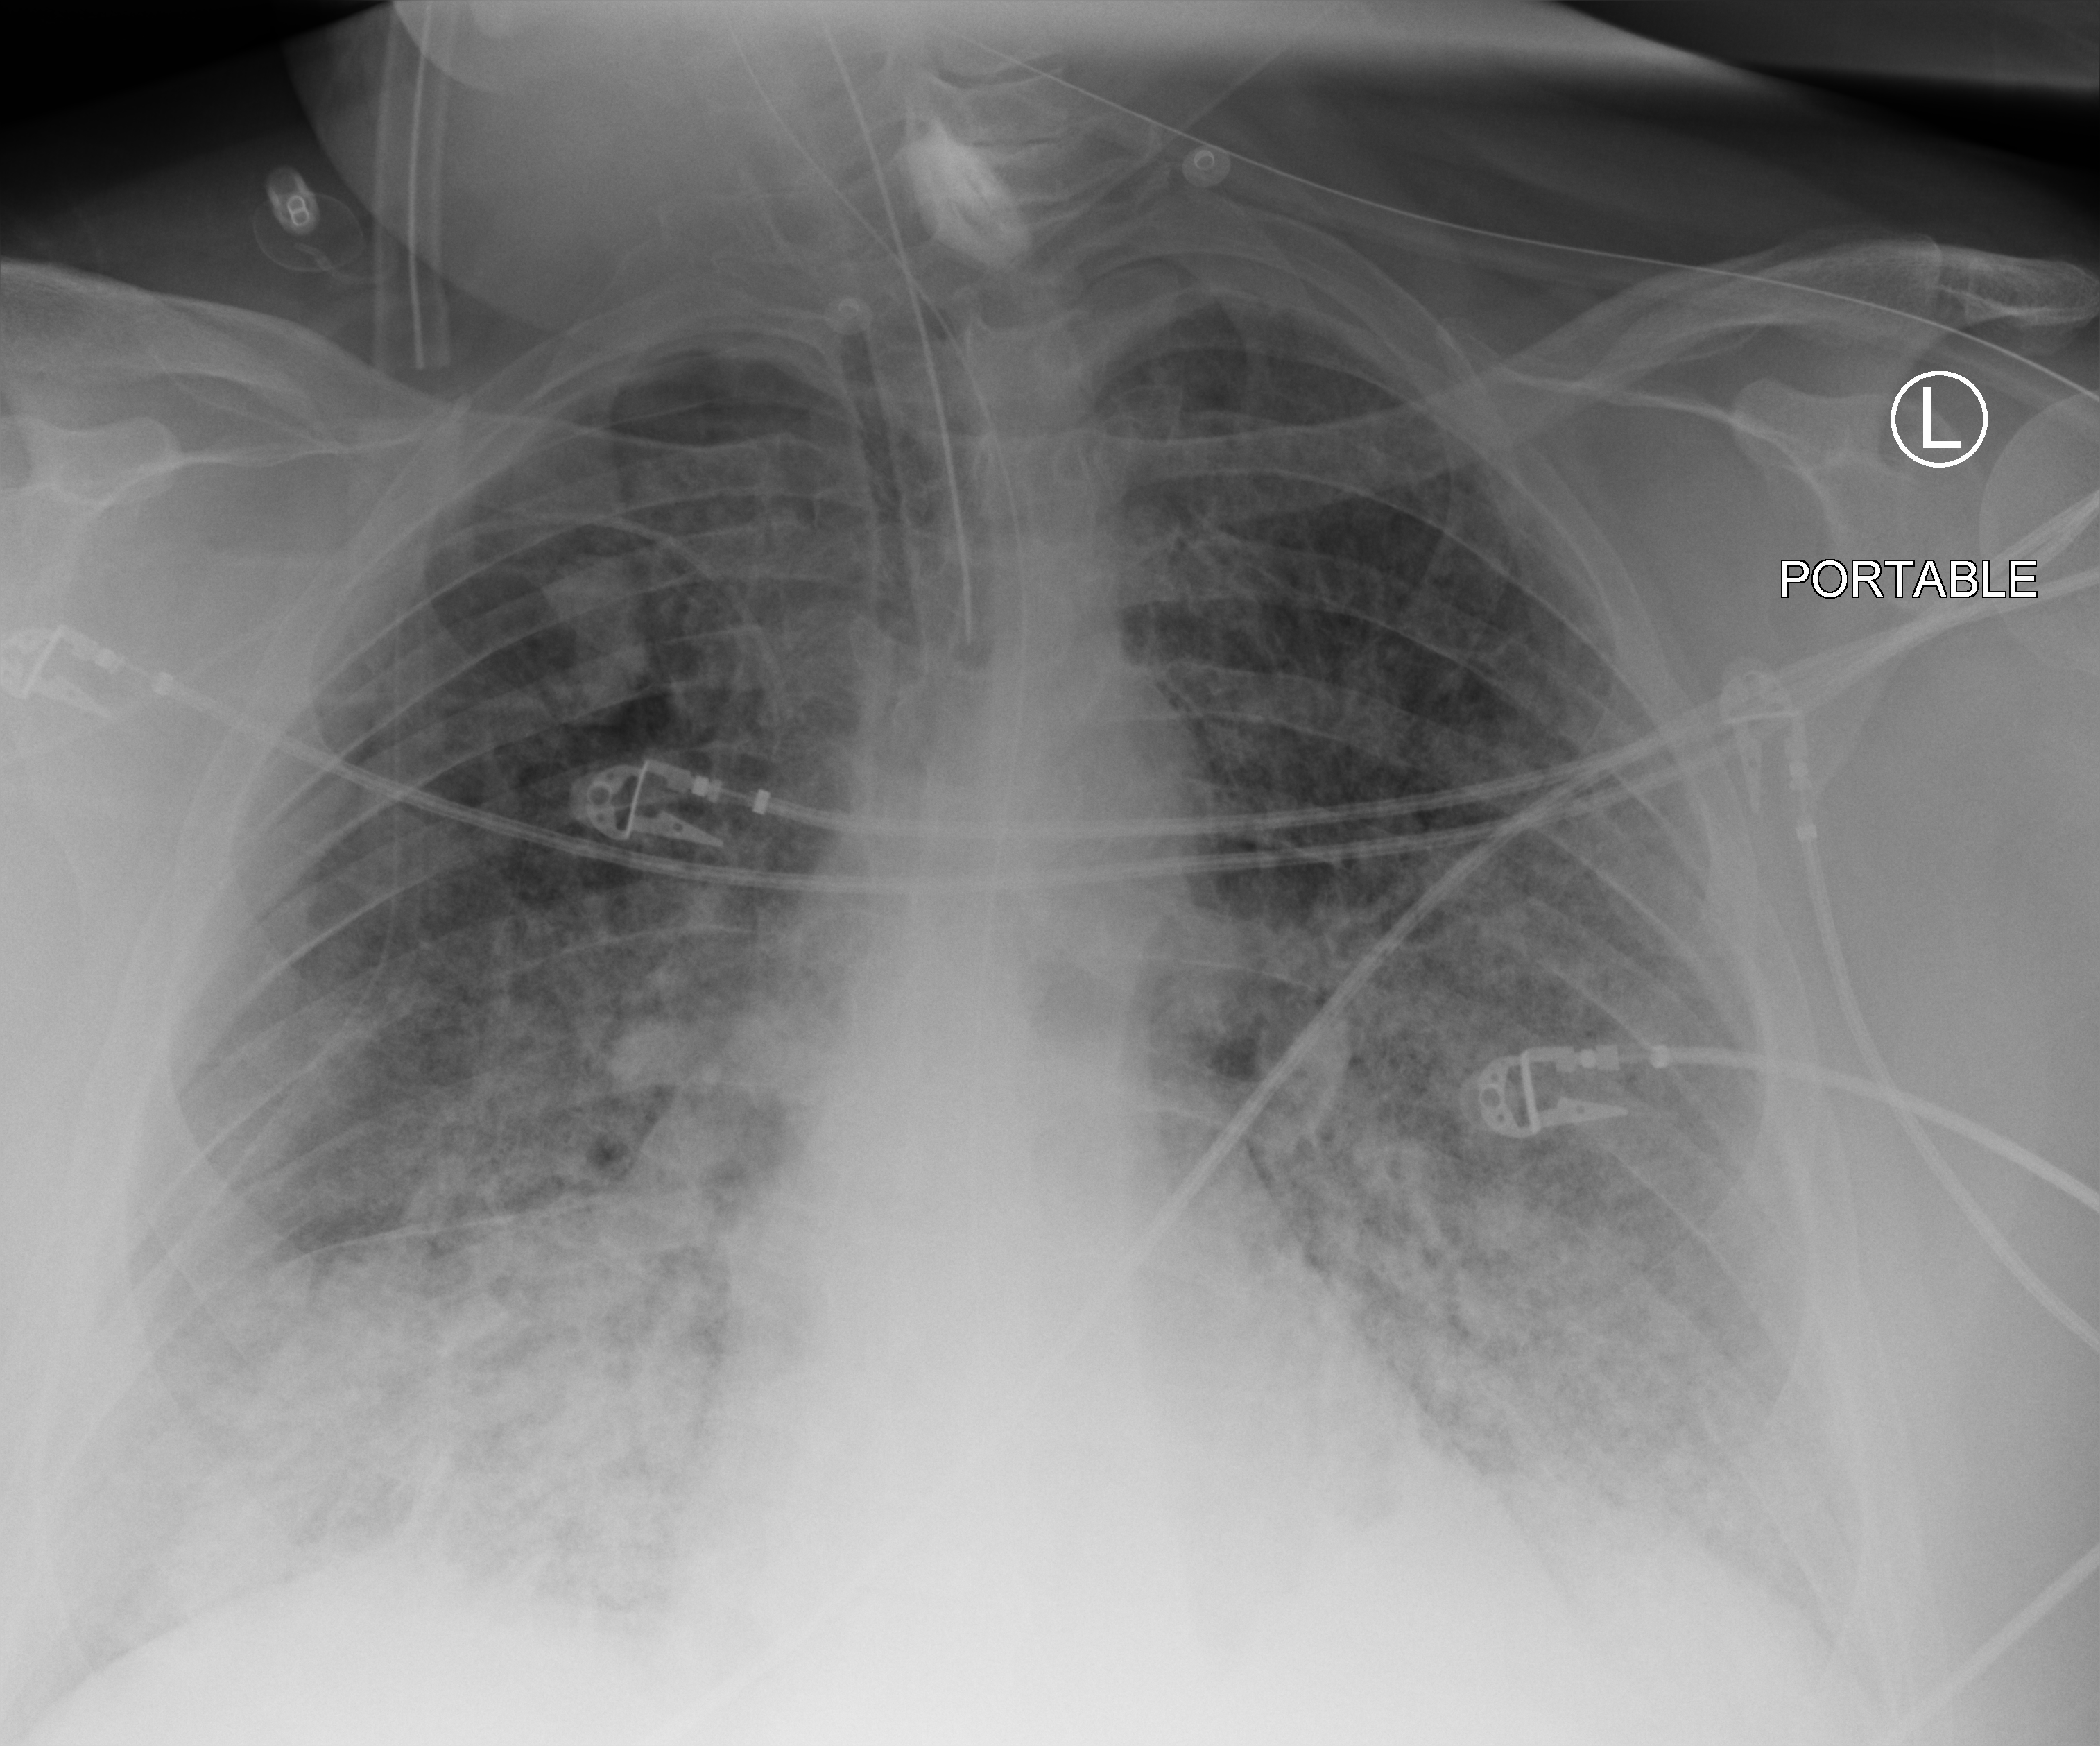
Portable chest radiograph, anteroposterior (AP) projection. Patient hospitalised with COVID-19; male, aged 60–74 years.
Hospital-stay facts (about this admission, not read from this image; timing relative to this image not recorded): length of hospital stay: 13 days.